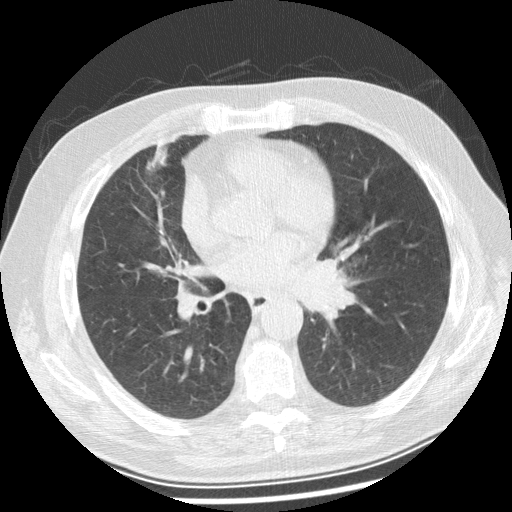
Low-dose screening chest CT, one axial slice; position 127 of 250 along the scan axis; reconstruction kernel STANDARD; lung window (W 1500 / L -600 HU); 2.5 mm slice thickness; 512 × 512 image matrix, field of view 360 × 360 mm.
Outlined on this slice (manually delineated by an expert):
- lesion 1 (tumor, left main bronchus): bounding box <293,259,356,319> (left, top, right, bottom; pixels)